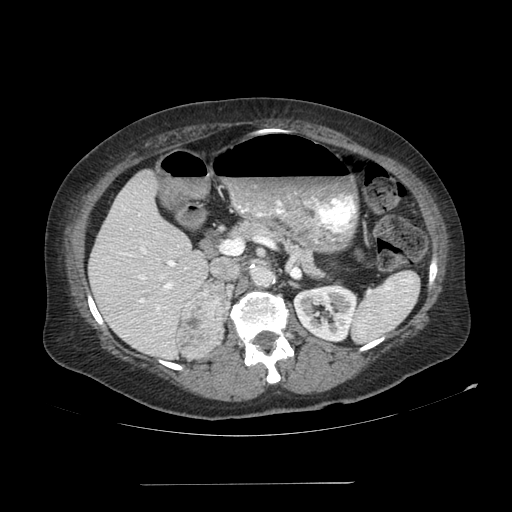
Contrast-enhanced abdominal CT, one axial slice. 120 kVp. Soft-tissue window (W 400 / L 40 HU). 512 × 512 image matrix, field of view 440 × 440 mm. Female patient, age 67 years. From the clinical record (not read from this slice): diagnosis: adrenocortical carcinoma; tumour side: right adrenal; tumour size at pathology: 9.8 cm; Ki-67 index: 59 %; stage (as recorded): 4.
Structures marked on this image (semi-automatic segmentation, software-assisted and operator-edited):
- mass: bounding box [x1, y1, x2, y2] px = [177, 280, 225, 357]